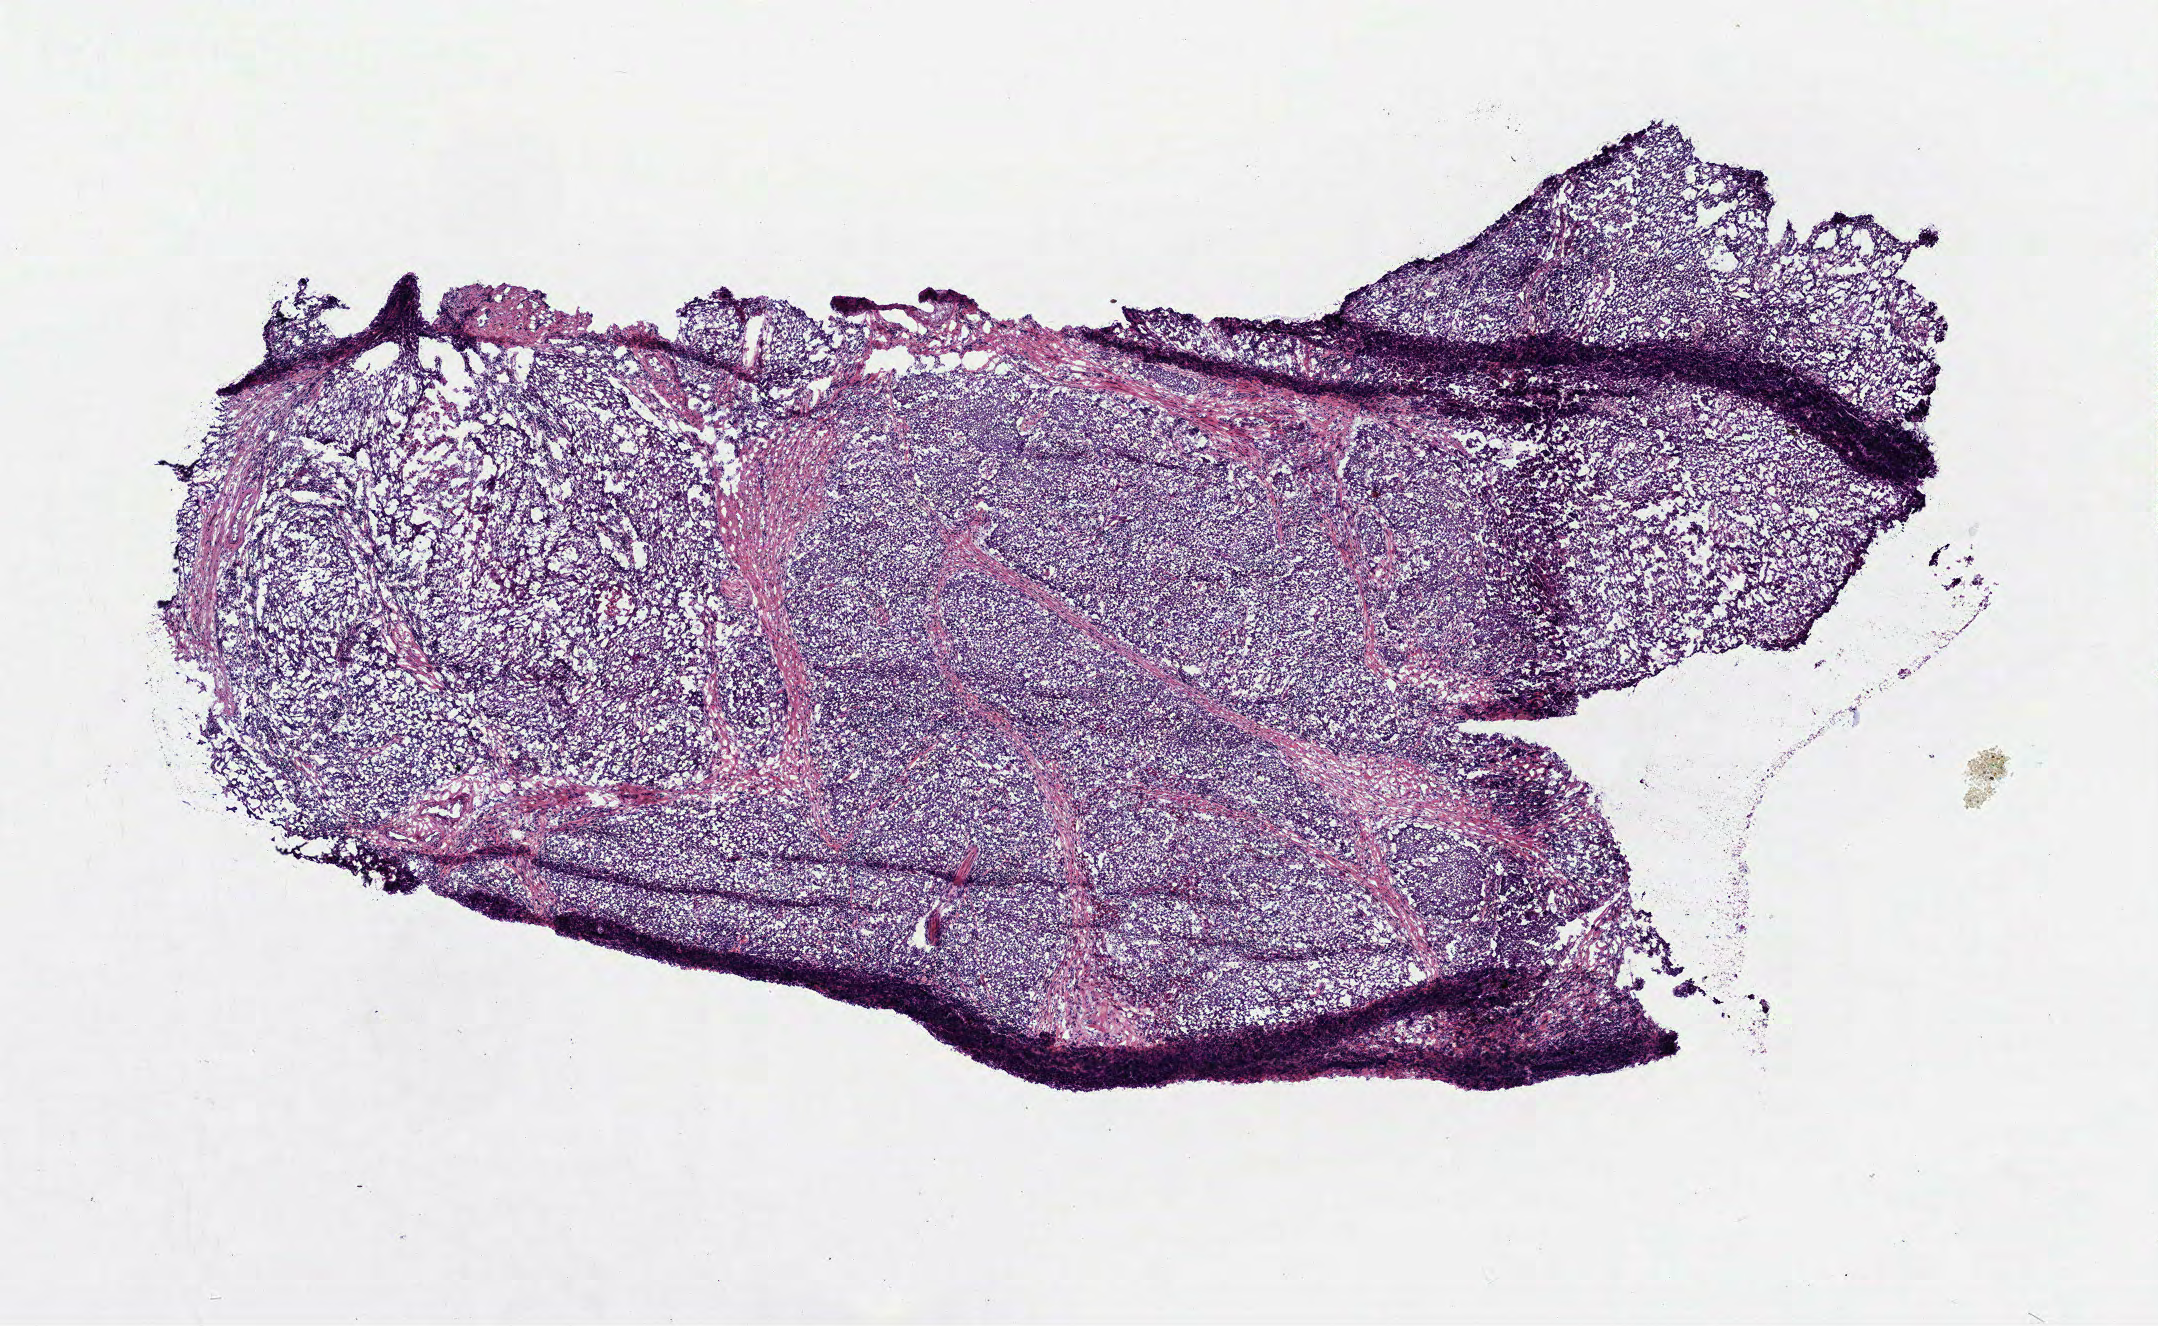
Whole-slide histology image, H&E — whole scanned area (about 8.7 x 5.3 mm, acquisition: 40x scan) shown as a low-resolution overview, frozen section, primary tumour sample from the head and neck. Male patient; age at initial diagnosis 73 years. Histologic grade: GX (grade cannot be assessed). Composition of this section per pathologist review: tumour cells 93%, tumour nuclei 75%, normal cells 0%, stromal cells 5%, necrosis 2%.
• histologic diagnosis: Squamous cell carcinoma, NOS (larynx, NOS)
• AJCC pathologic stage: IVA (6th edition)
• laterality: right